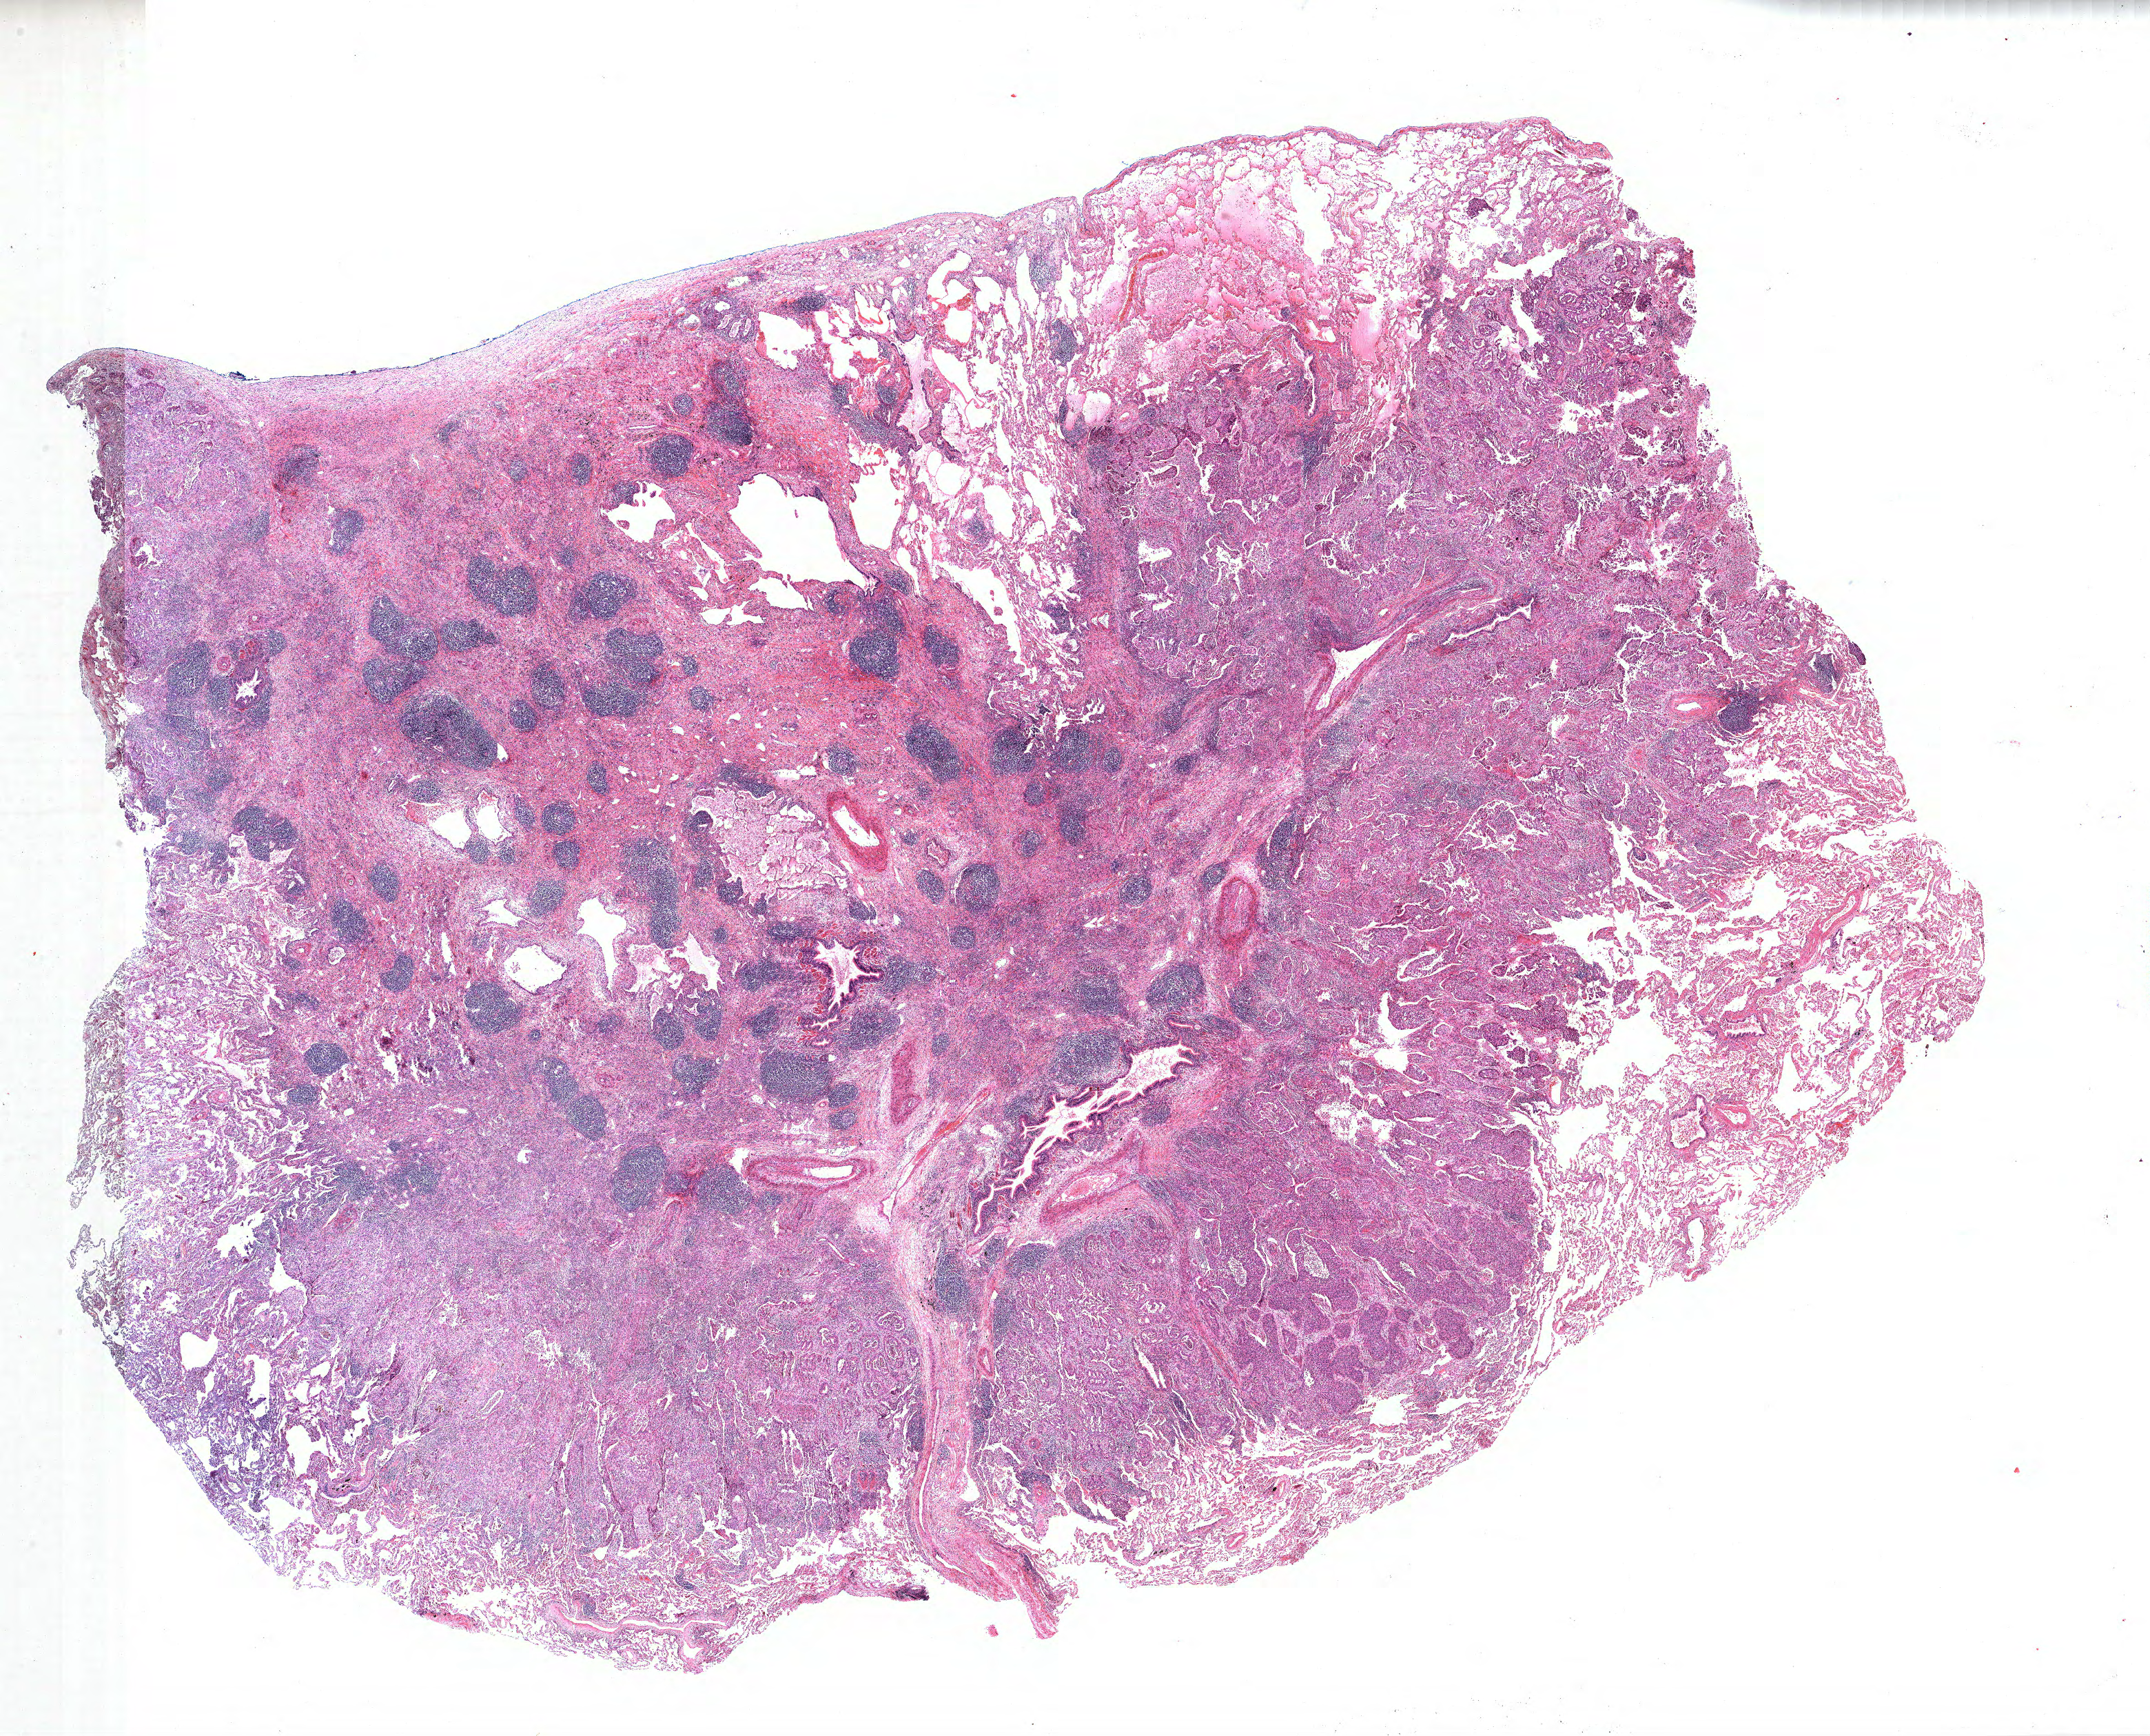
H&E whole-slide image, whole scanned area (about 25.0 x 20.2 mm, slide scanned at 40x) shown as a low-resolution overview, formalin-fixed paraffin-embedded (FFPE) section, lung. Female patient, aged 68 at enrolment. Current smoker at enrolment. Grade: moderately differentiated (G2).
Participant's lung-cancer diagnosis: Adenocarcinoma, NOS (ICD-O-3 8140/3). Stage (AJCC 6th edition): IB. Primary tumour location (clinical record): left lower lobe. Tumour size (pathology): 40 mm.